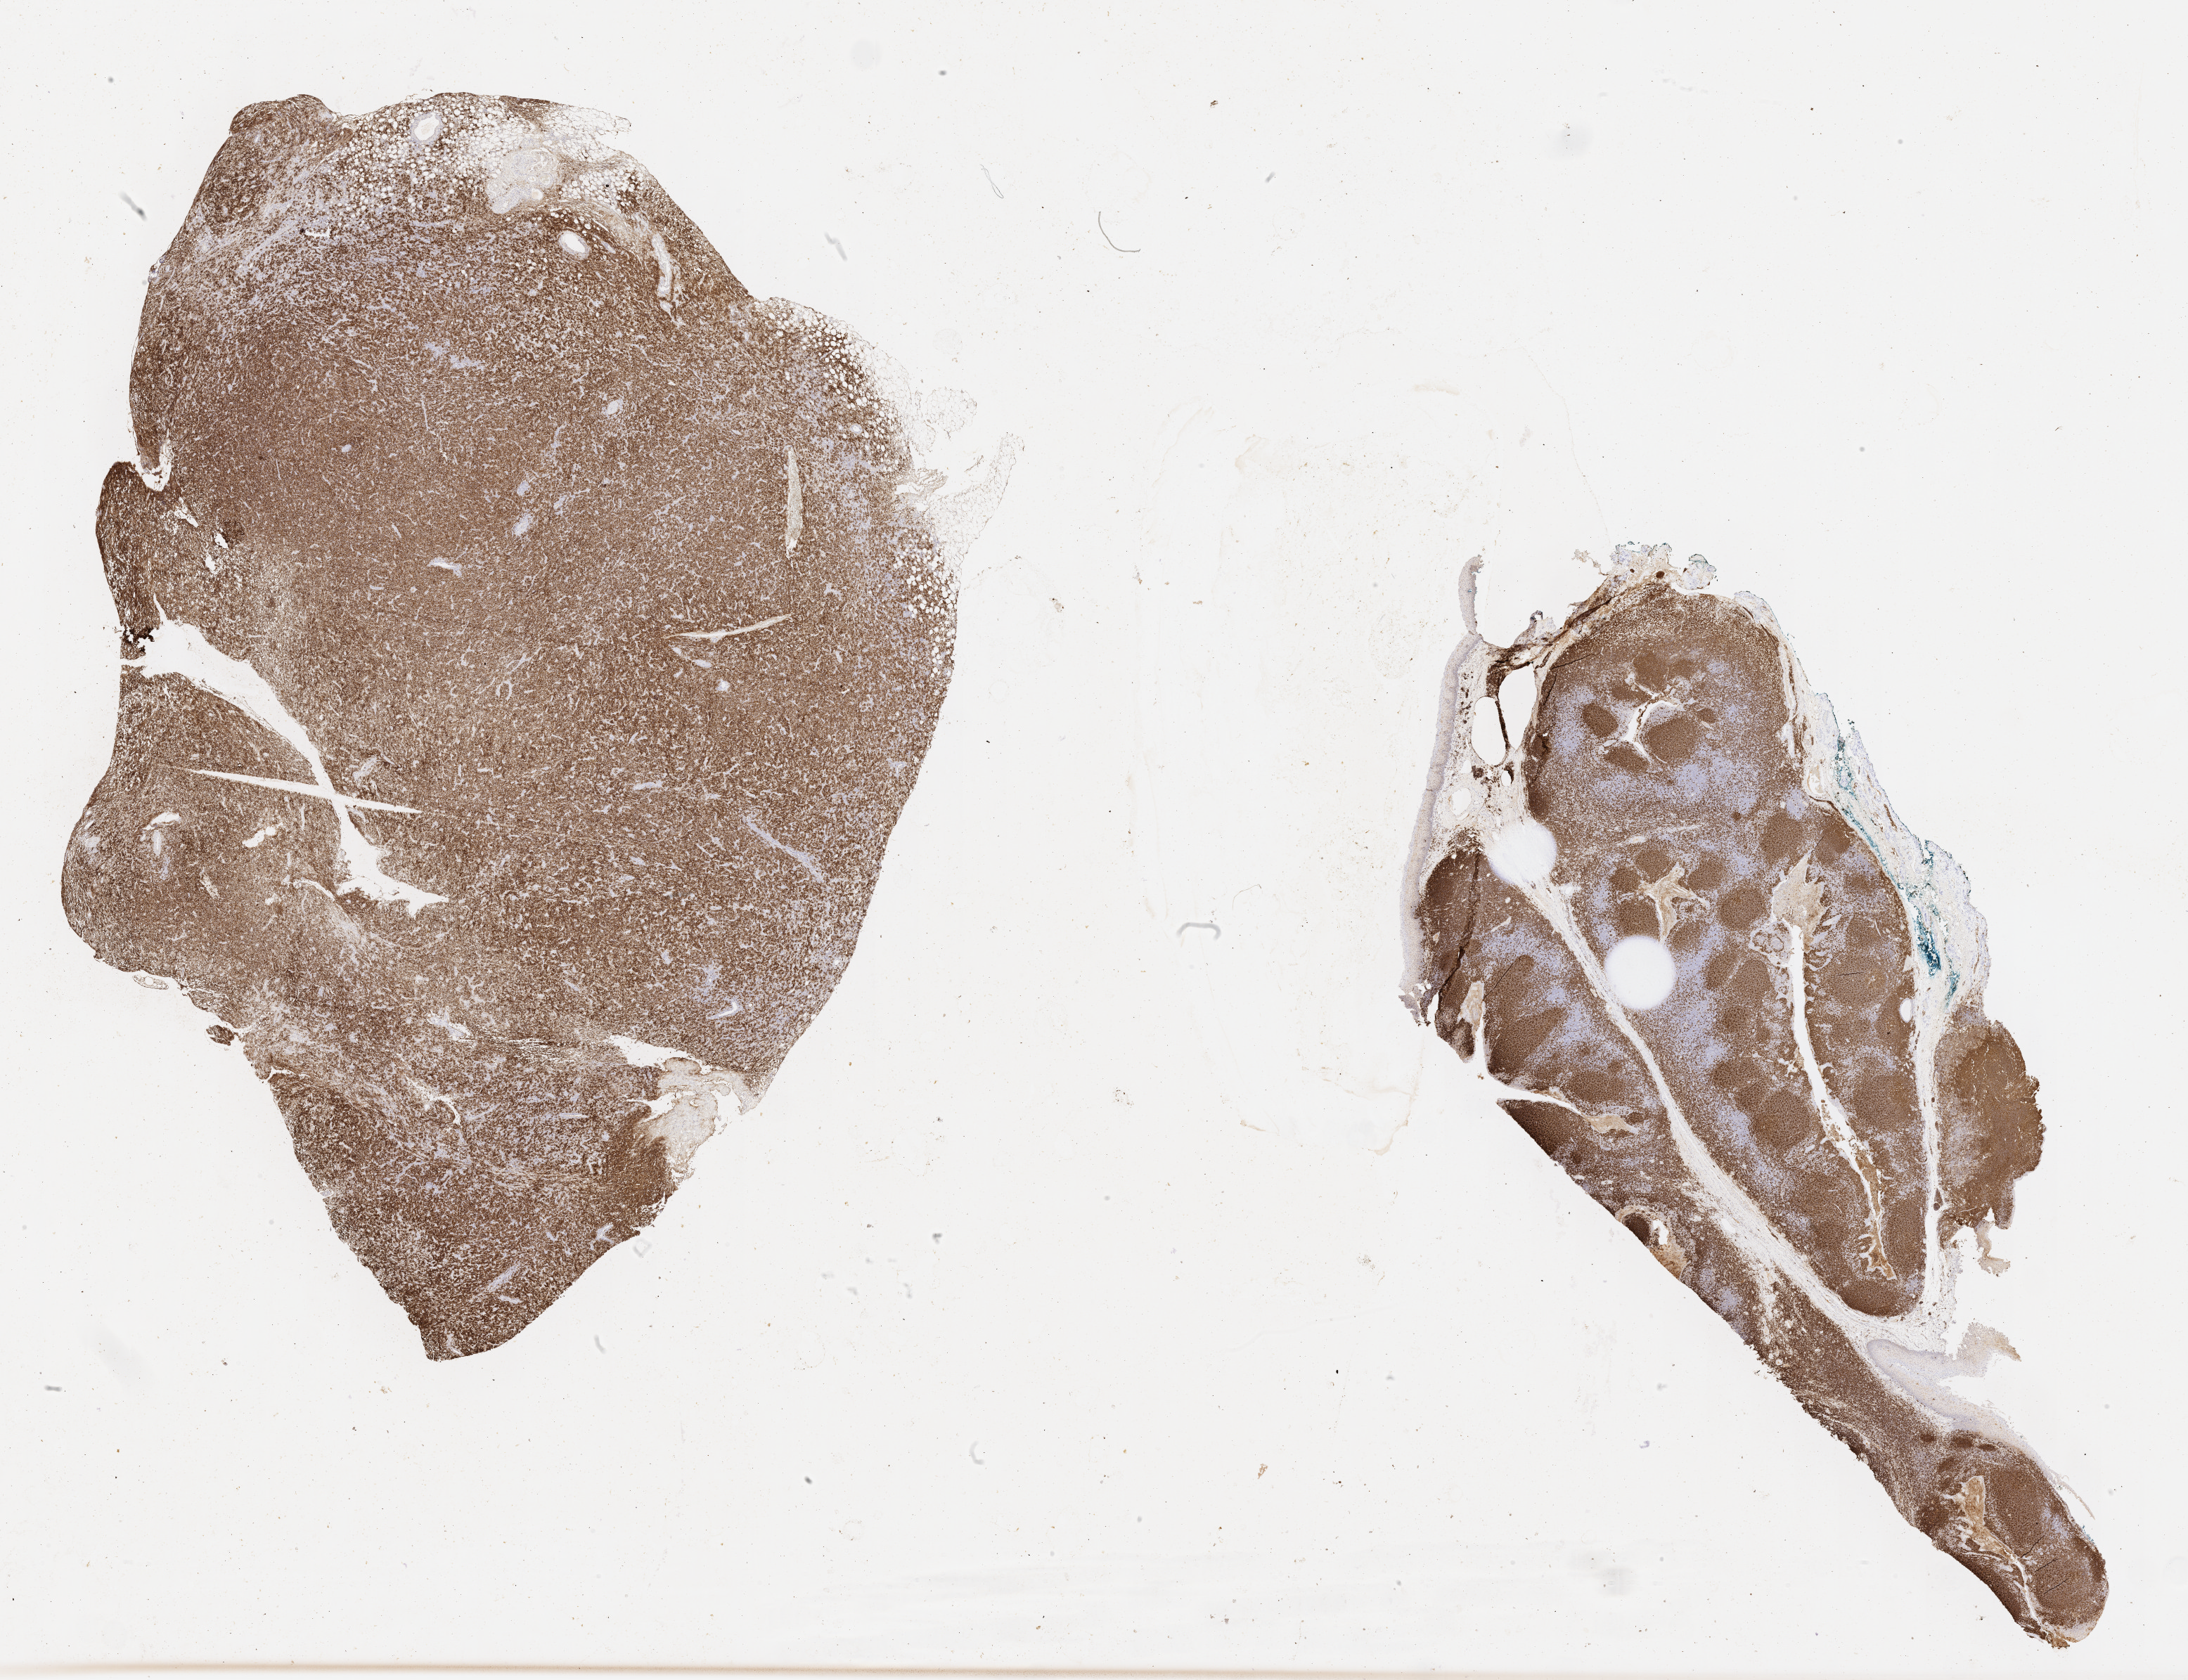
IHC for CD20, whole-slide image, low-resolution overview of the scanned area, about 25.2 x 19.3 mm. Patient sex: female.
Specimen: tumor tissue.